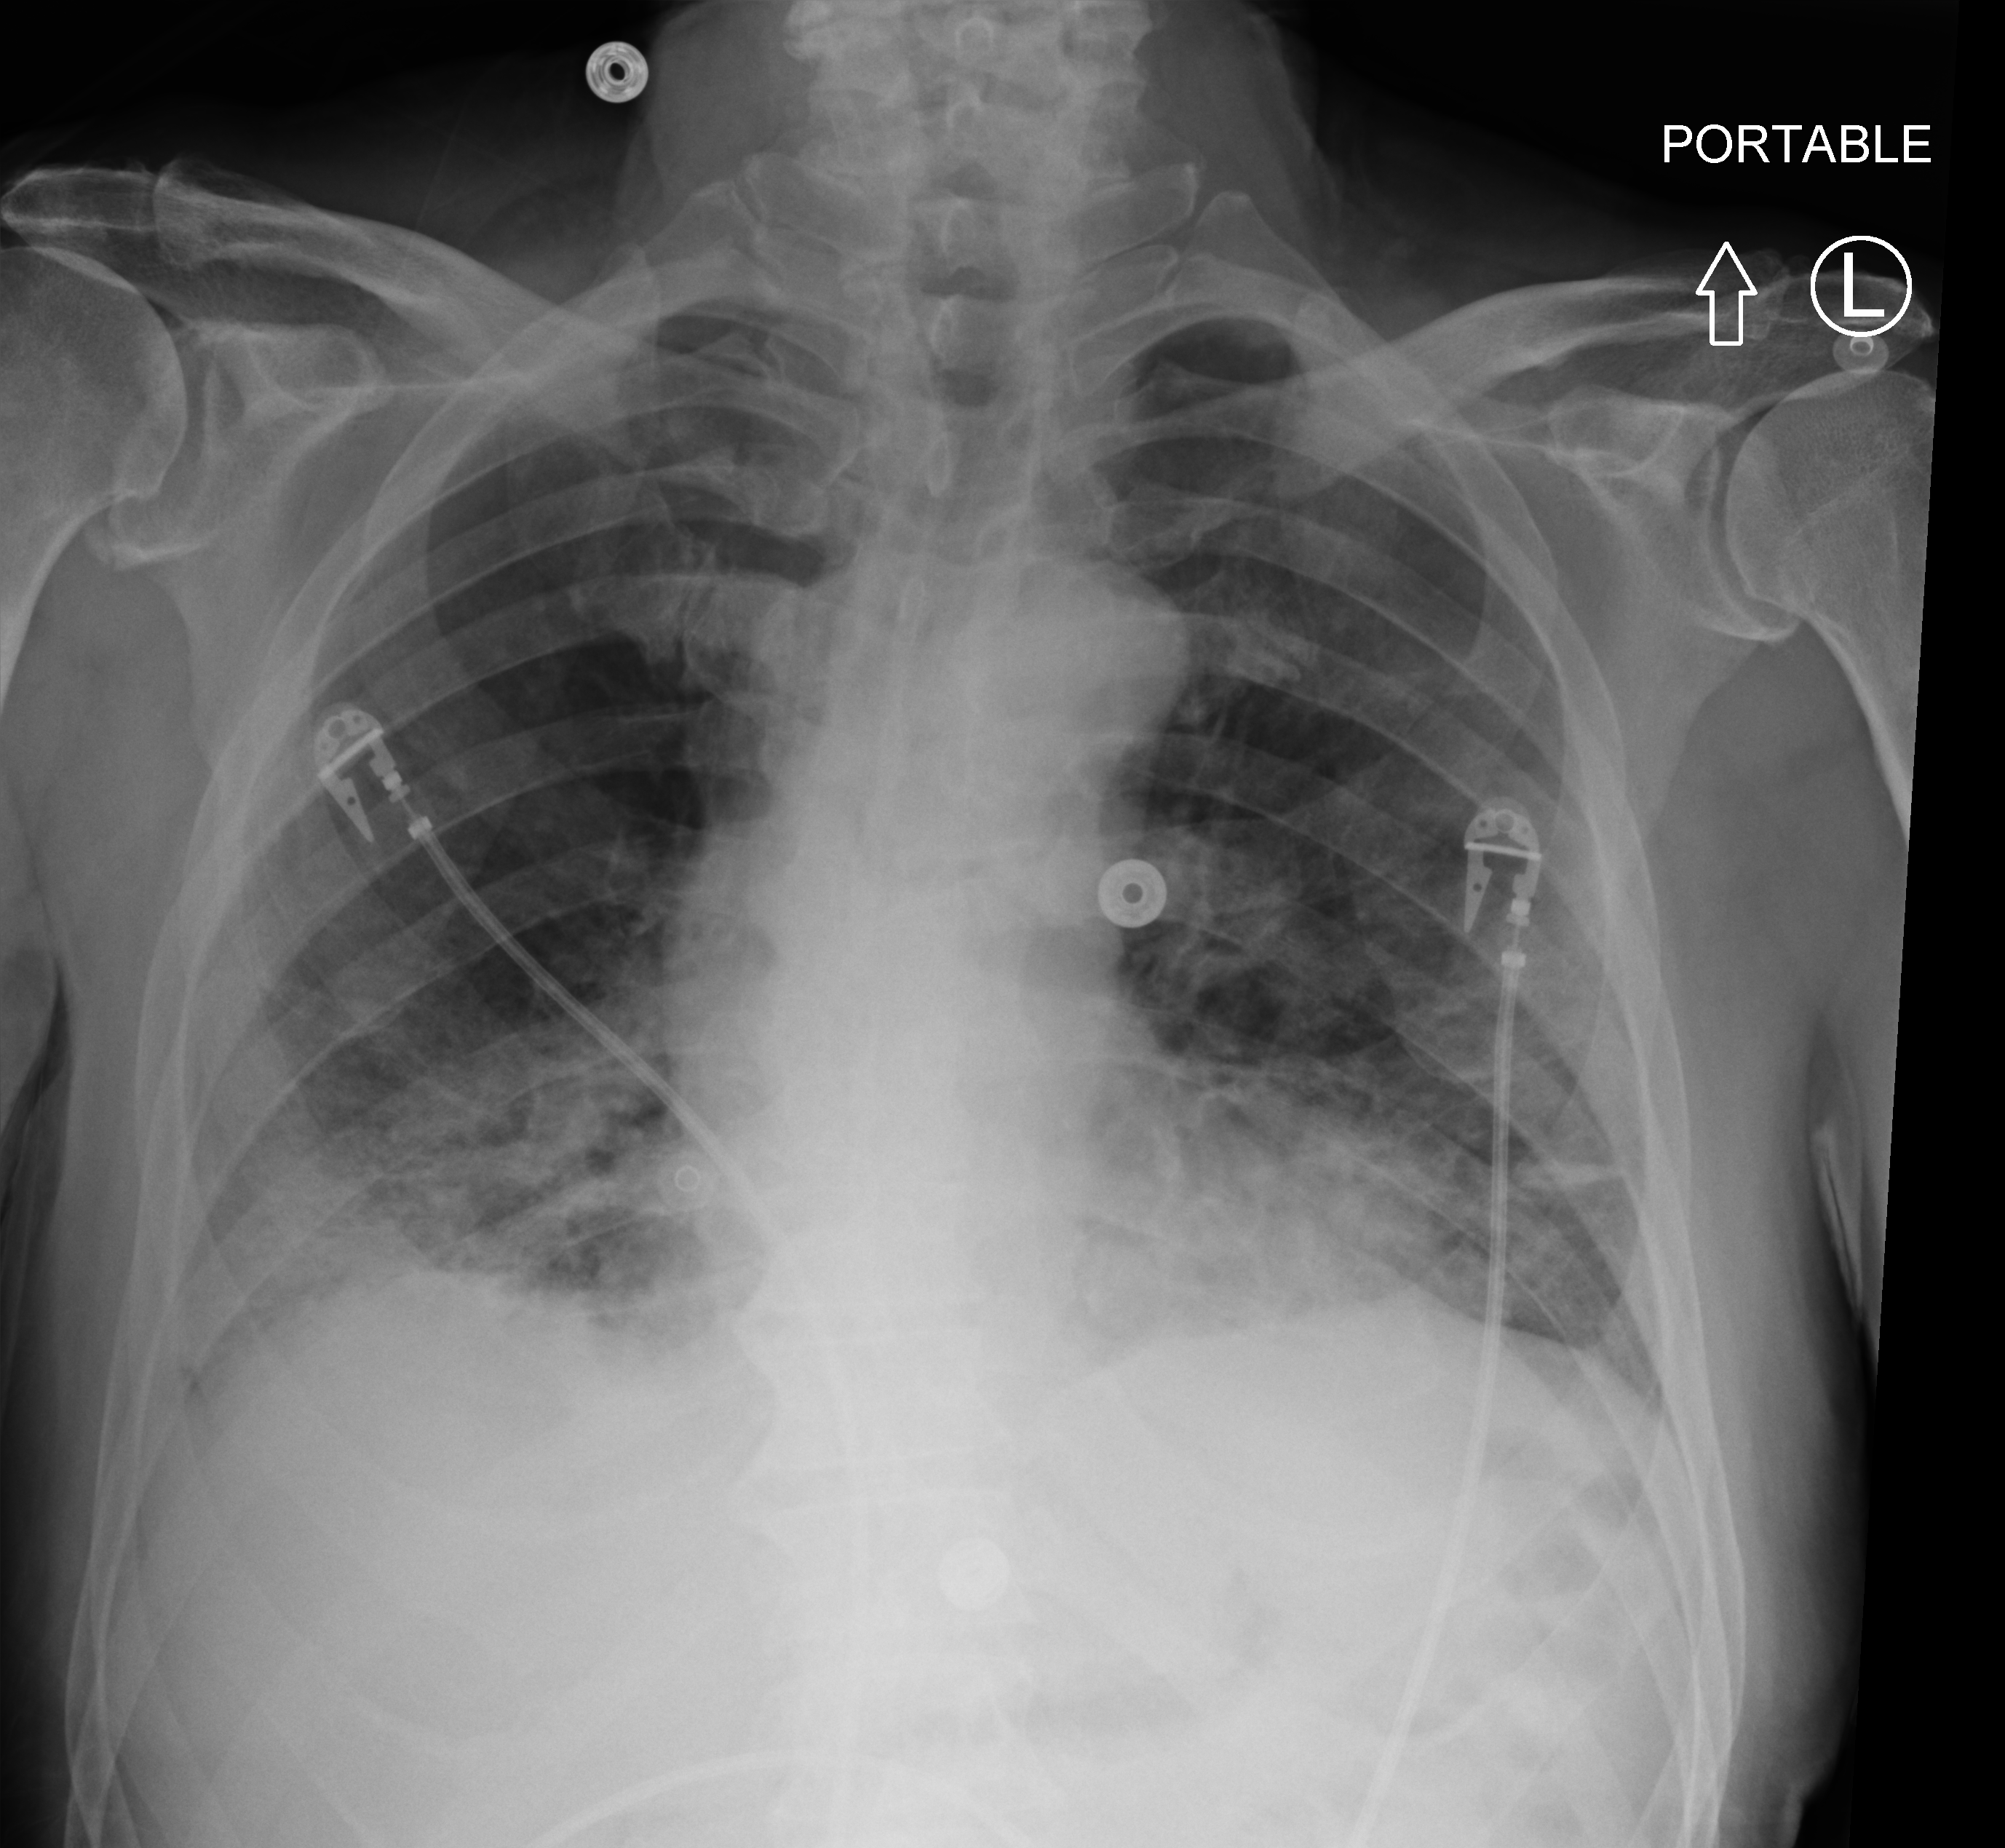
Bedside chest radiograph (computed radiography); anteroposterior (AP) projection. Patient hospitalised with COVID-19; male, aged 75–90 years.
Hospital-stay facts (about this admission, not read from this image; timing relative to this image not recorded):
- diabetes (admission record): no
- hypertension (admission record): no